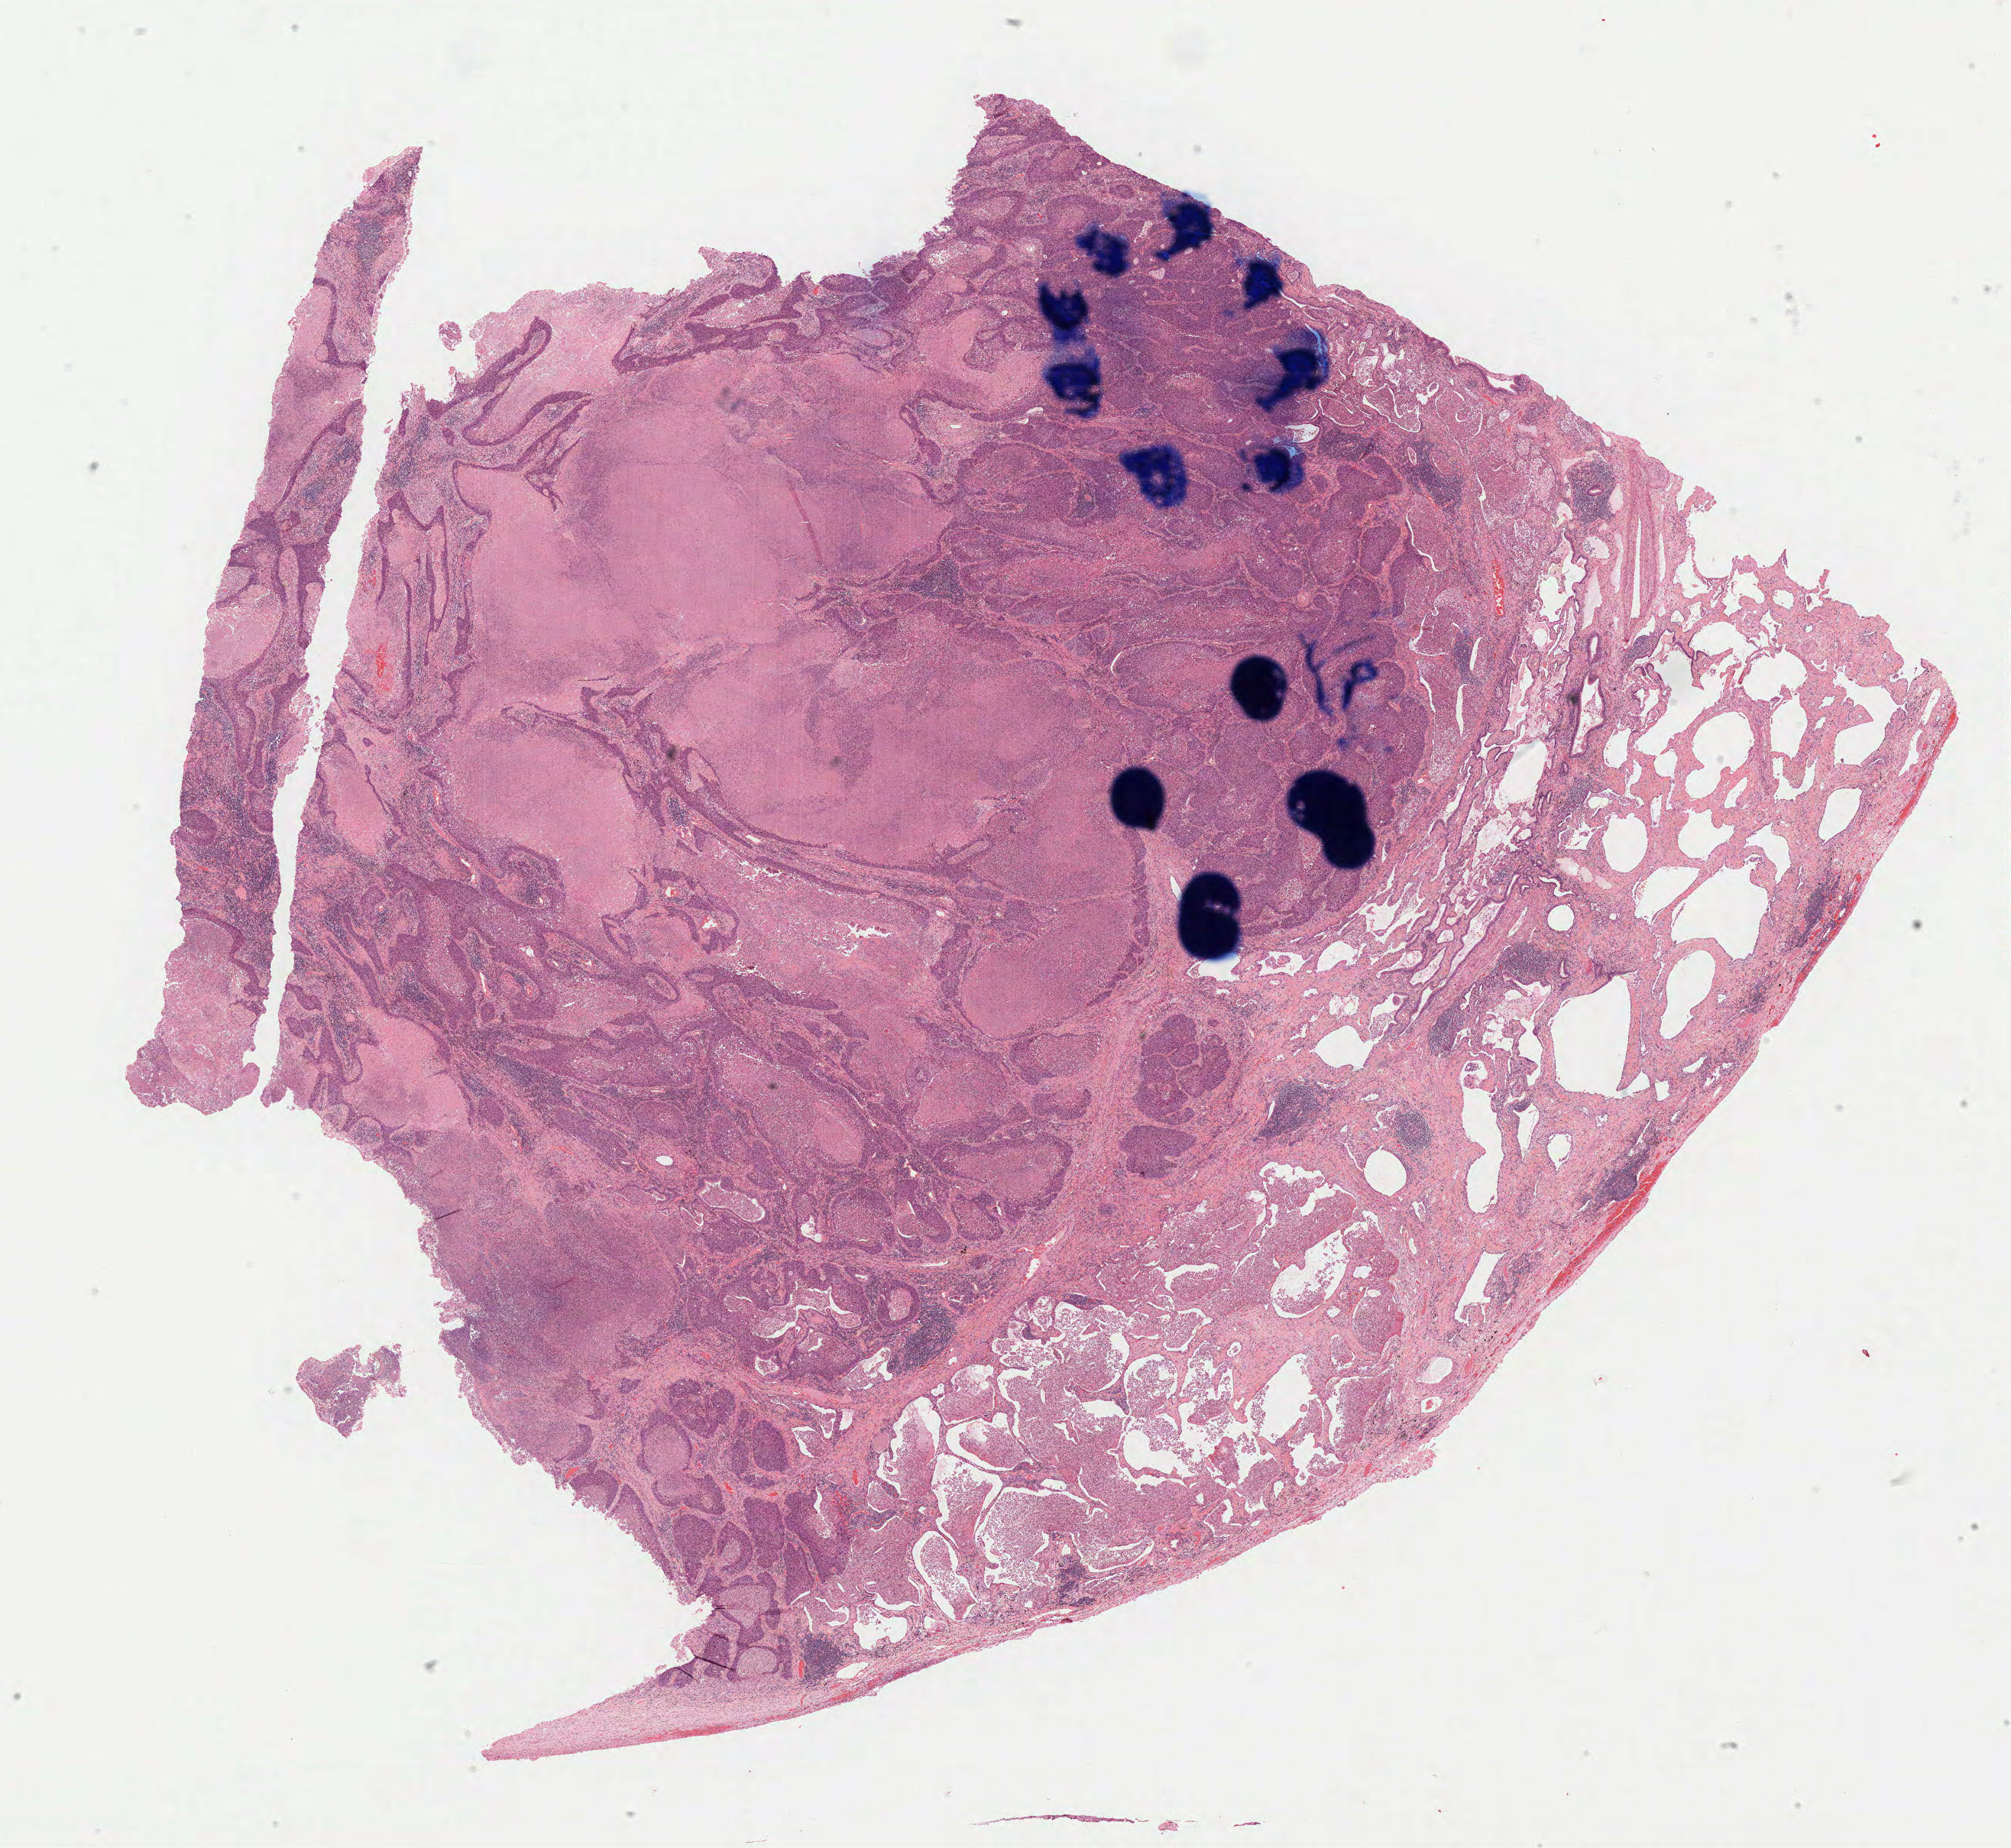
H&E whole-slide image, low-resolution overview of the scanned area, about 21.2 x 19.5 mm (slide scanned at 40x); formalin-fixed paraffin-embedded (FFPE) diagnostic section; primary tumour sample from the lung. Male, age 65 years at initial diagnosis.
Histologic diagnosis: Squamous cell carcinoma, NOS. AJCC pathologic stage: IB.